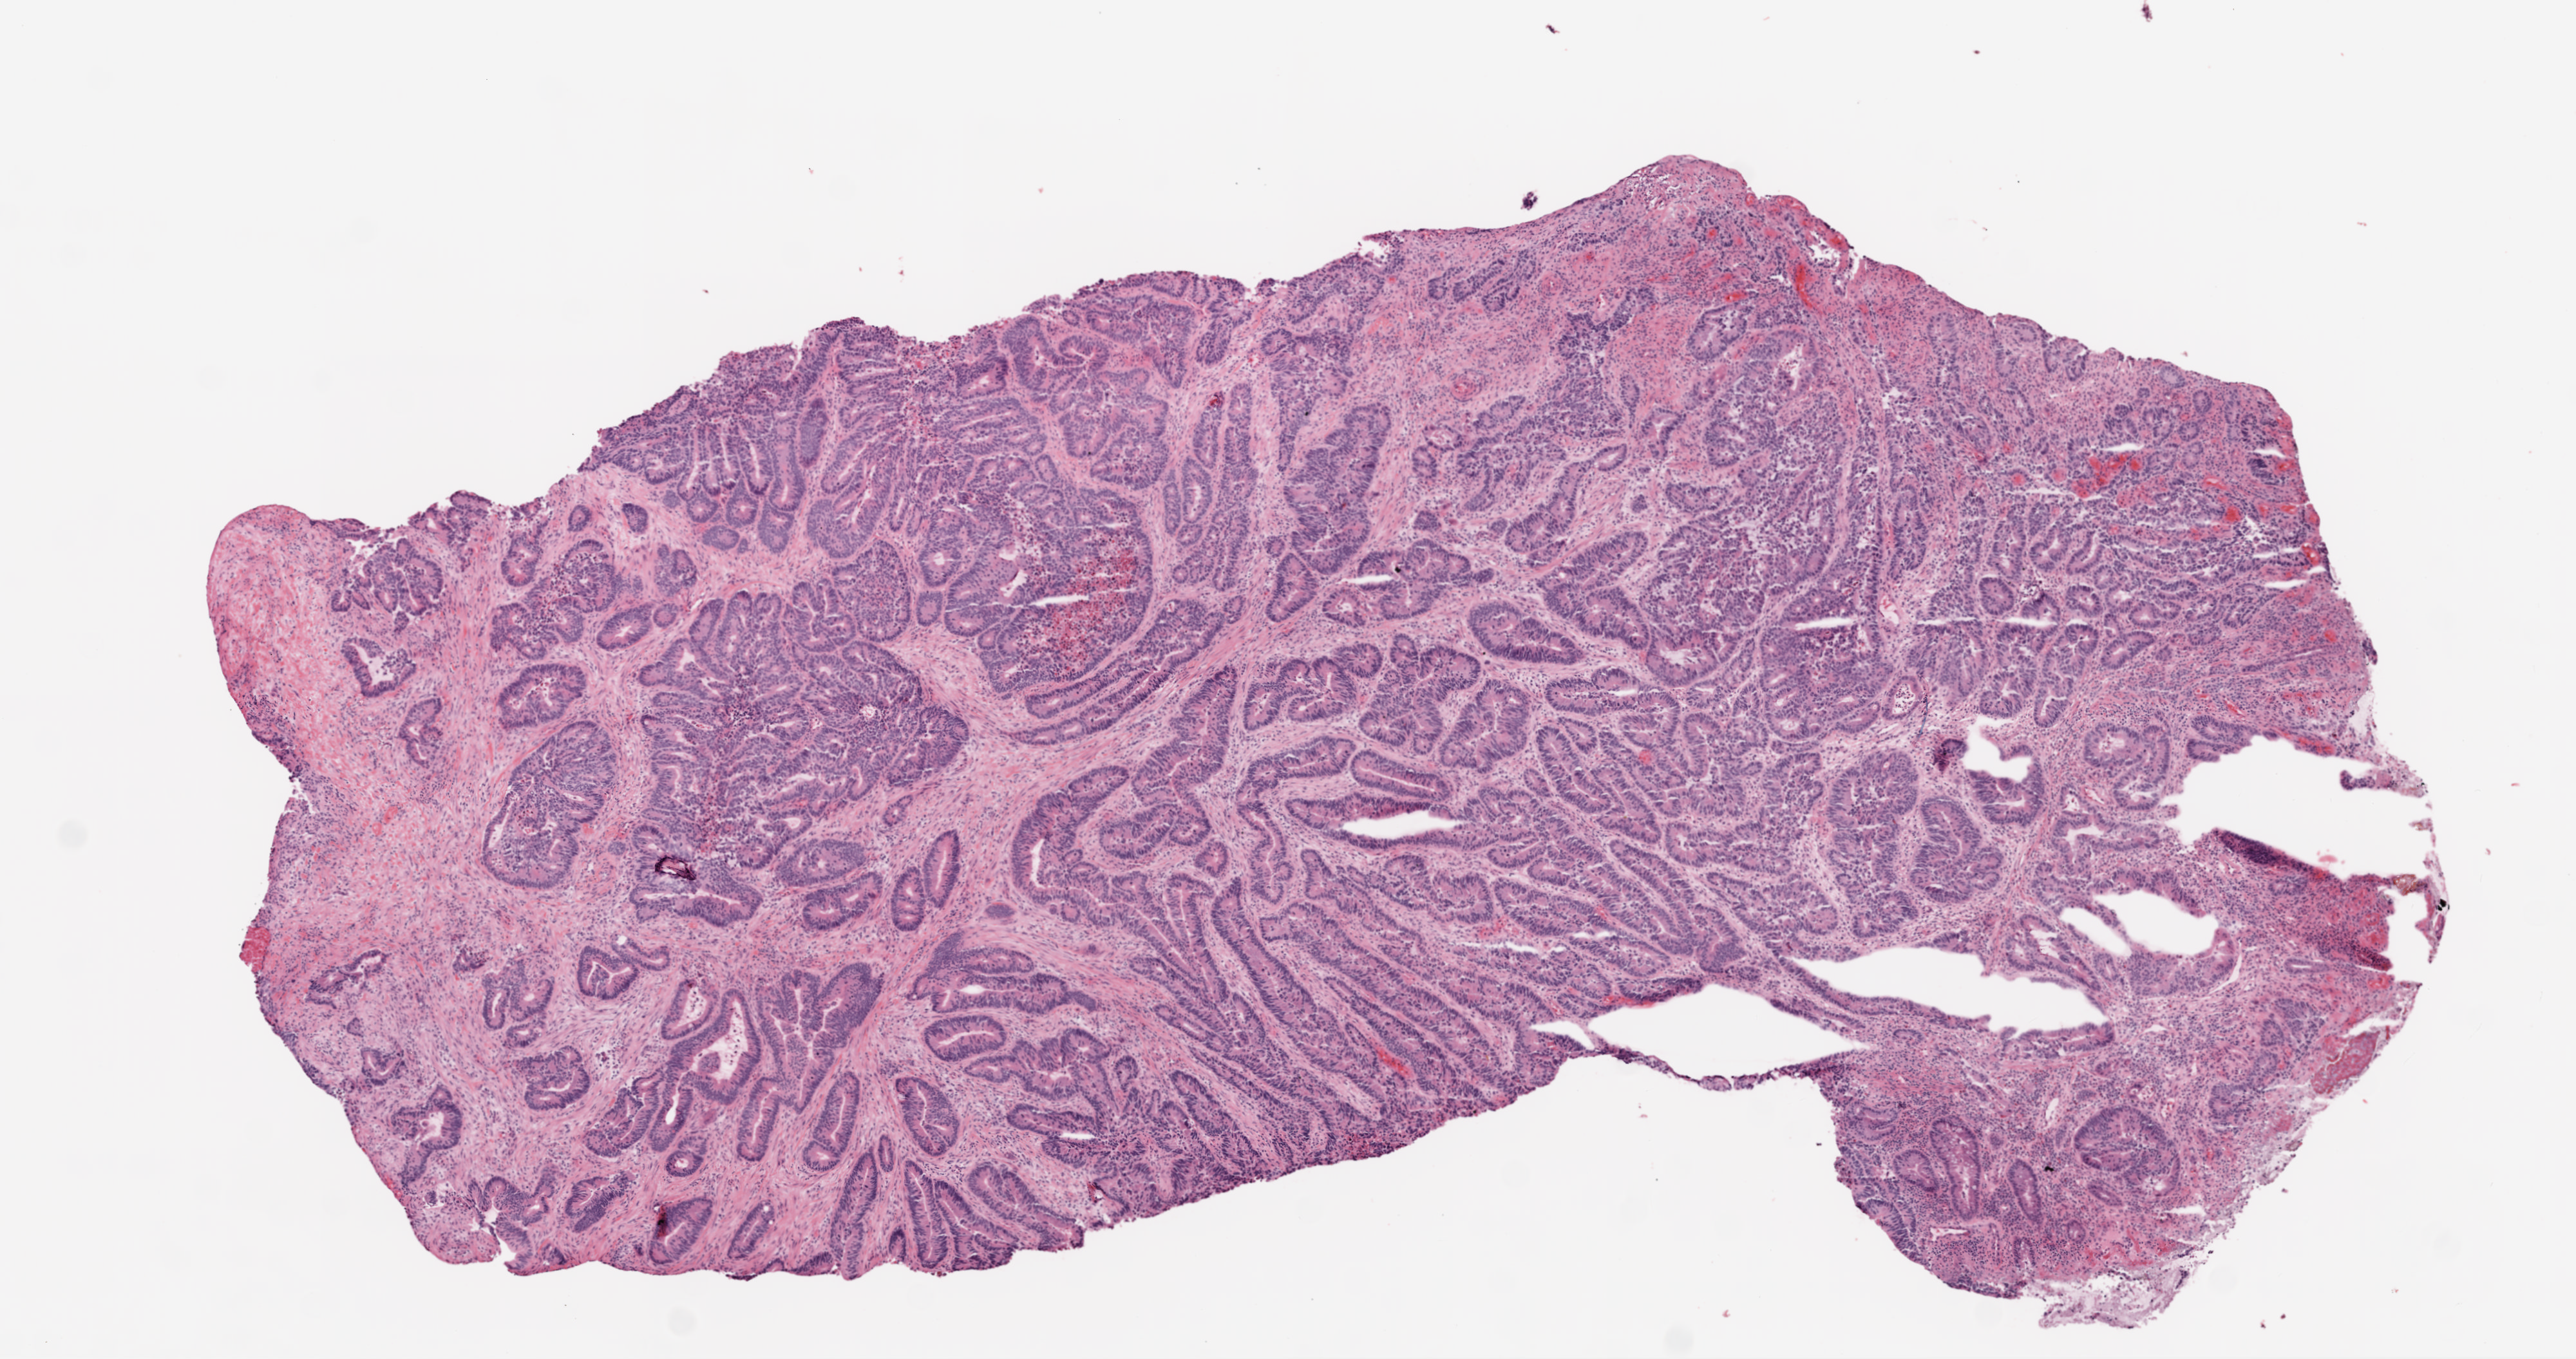
Digitized H&E-stained tissue section (whole slide), low-resolution overview of the scanned area, about 8.0 x 4.2 mm, frozen section from the top of the tissue portion, sample: primary tumour, rectum. Female patient; age at initial diagnosis 79 years. Composition of this section per pathologist review: tumour cells 60%, tumour nuclei 75%, normal cells 15%, stromal cells 20%, necrosis 5%.
- diagnosis: Adenocarcinoma, NOS
- lymph nodes positive (case pathology): 2 of 14 examined